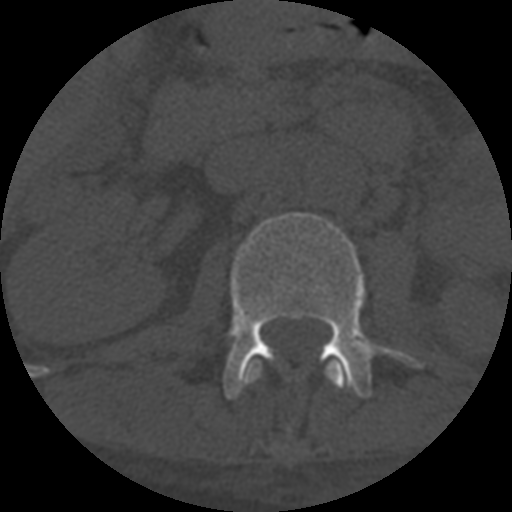
CT including the spine, one axial slice; slice 268 of 708 in the series (ordered by position); one of 3 acquisitions stored at this slice position; bone window (W 1800 / L 400 HU); 1.25 mm slice thickness; 512 × 512 image matrix. Patient age 55 years. Case-level facts recorded for this patient, not image findings: primary cancer: colon; vertebrae with lytic lesions (as recorded): T12, L1, L5.
Outlined on this slice (semi-automatic segmentation, software-assisted and operator-edited):
- L1 vertebra: bounding box [x1, y1, x2, y2] px = [243, 359, 347, 389]
- L2 vertebra: [223, 212, 423, 400]